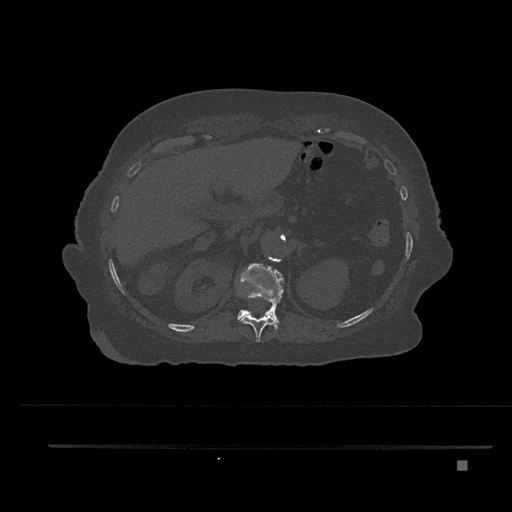
CT including the spine, one axial slice. Slice 290 of 797 in the series (ordered by position). 120 kVp. Bone window (W 1800 / L 400 HU). 0.5 mm slice thickness. 512 × 512 image matrix, field of view 437 × 437 mm. Female patient, age 76 years. From the clinical record (not read from this slice): primary cancer: lung.
Outlined on this slice (semi-automatically segmented with operator editing):
- T11 vertebra: box from (x=238, y=293) to (x=277, y=342) px
- T12 vertebra: (x=236, y=263)–(x=284, y=330)